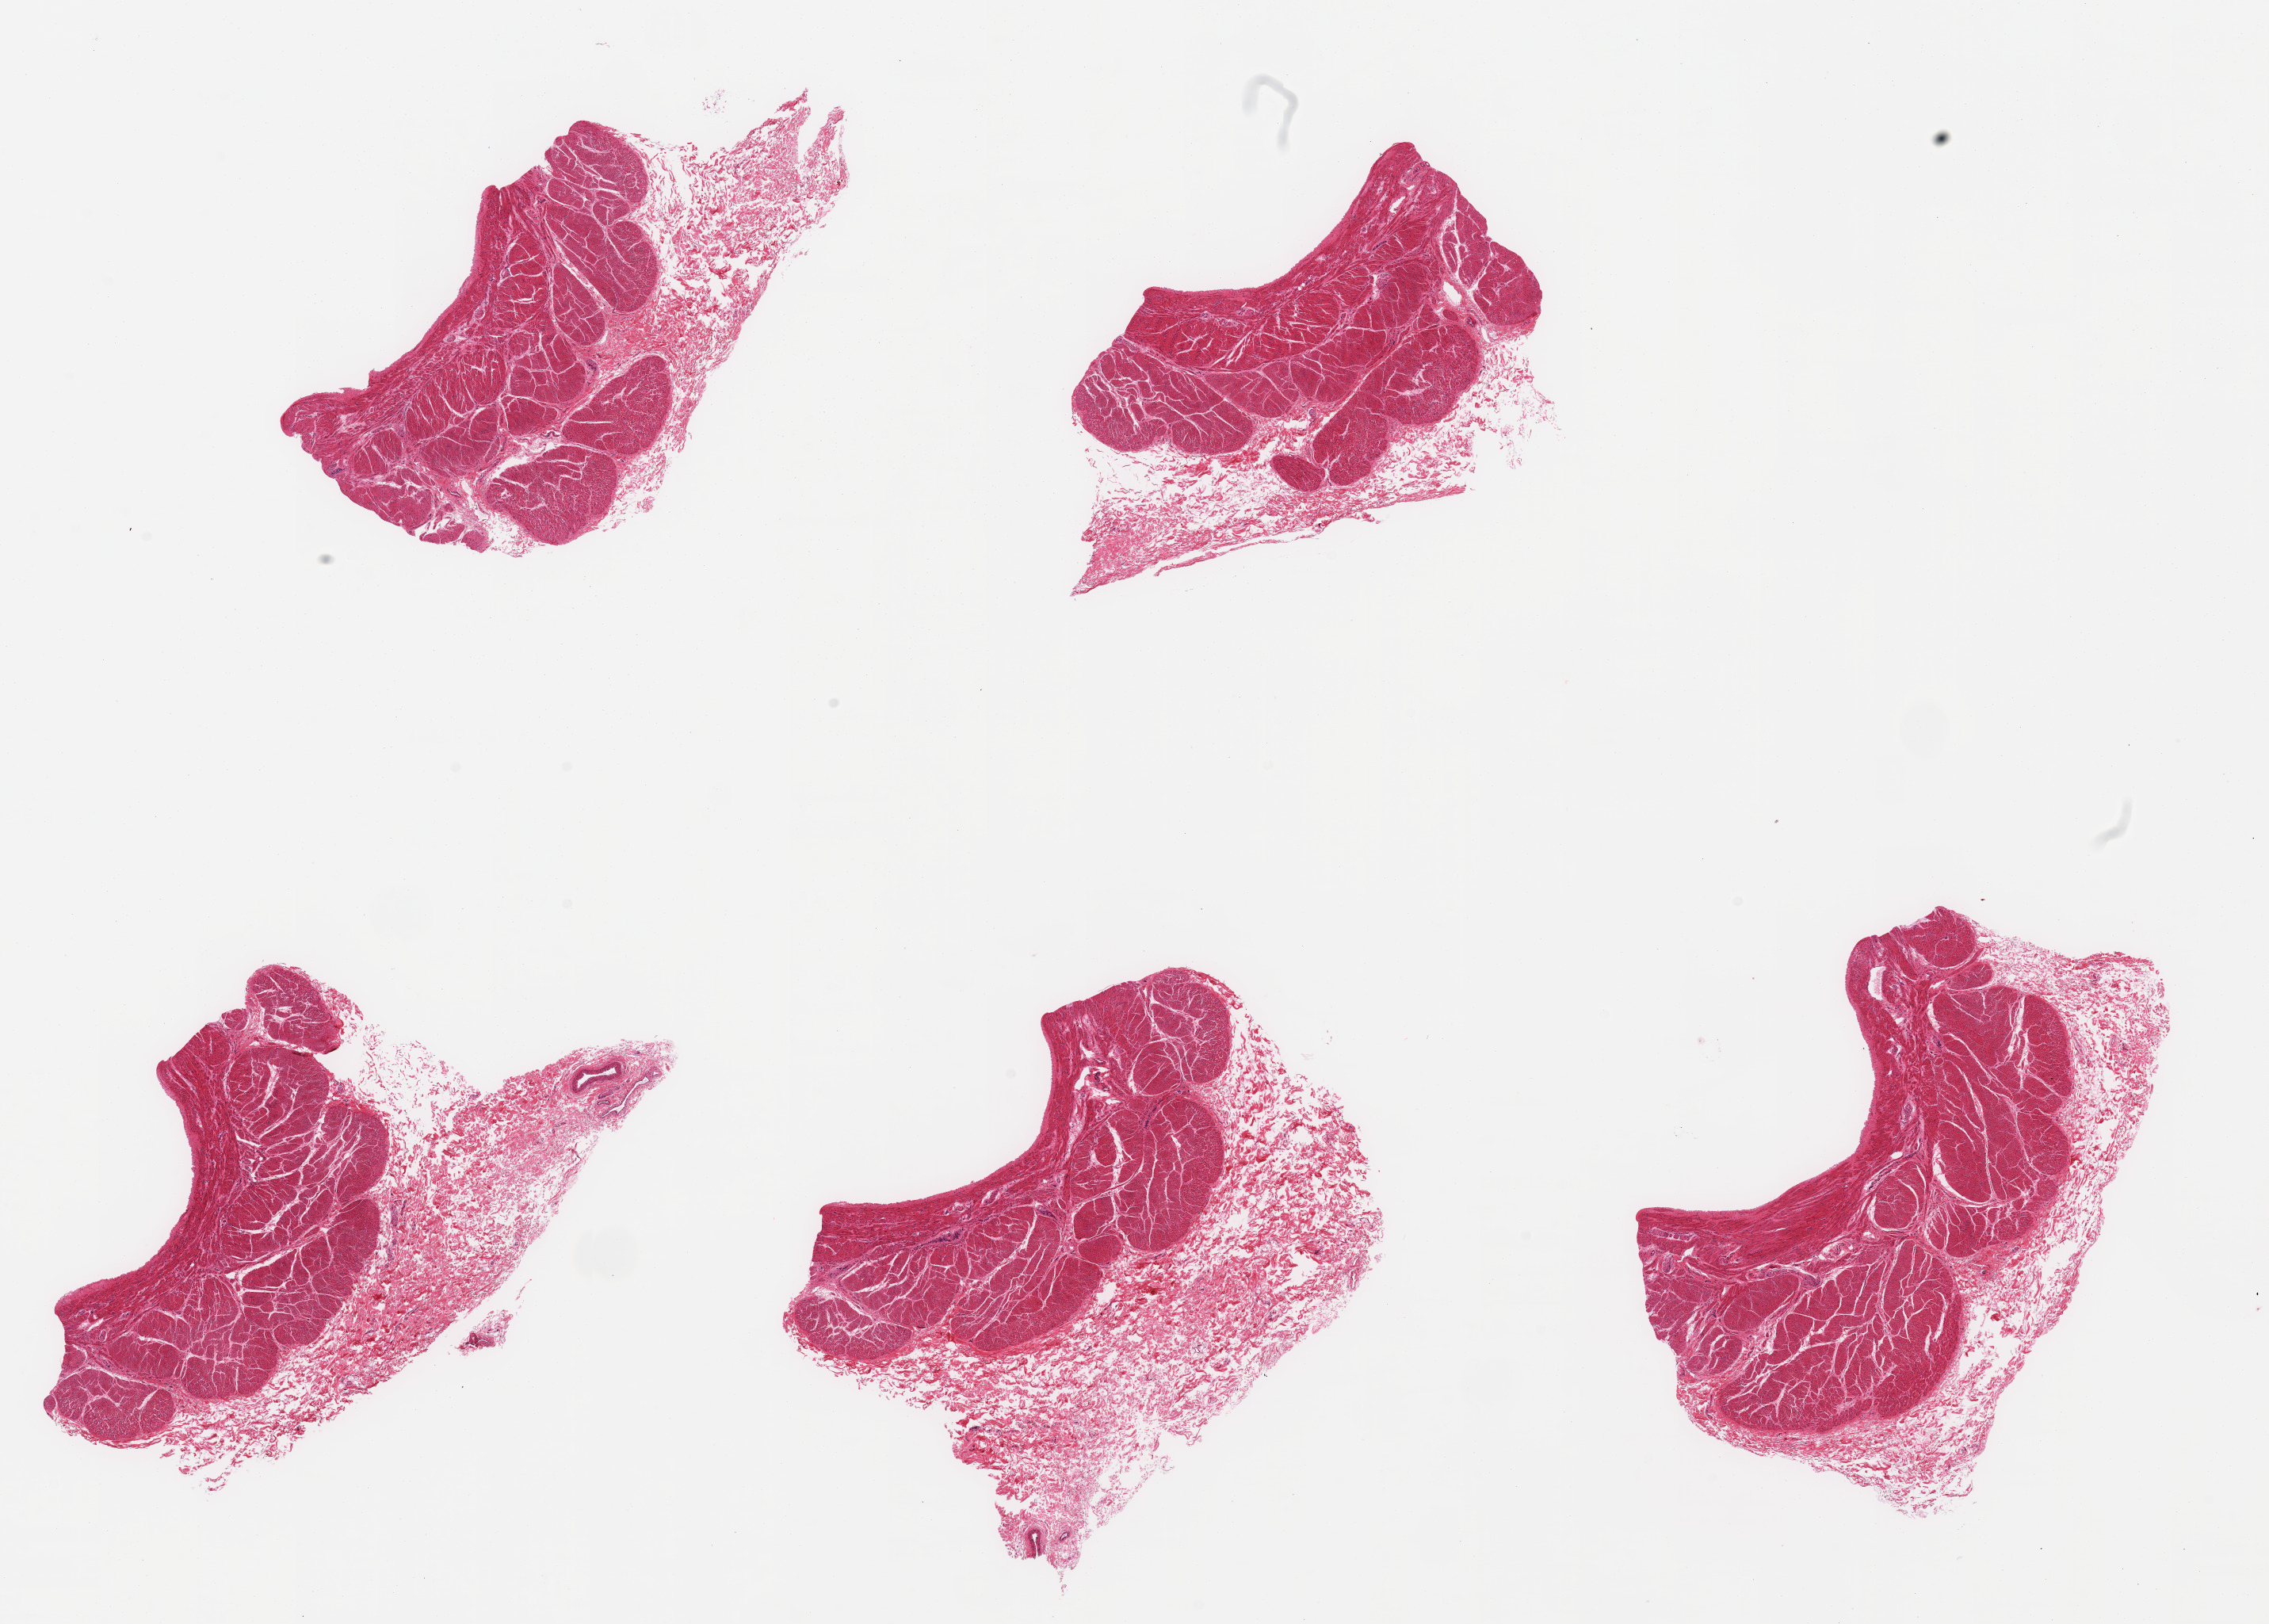
Whole-slide image, haematoxylin and eosin stain, brightfield, shown as a low-resolution overview of the whole scanned area (about 22.6 x 16.2 mm, acquisition: 20x scan); PAXgene-fixed, paraffin-embedded tissue; target tissue: stomach; donor tissue sample. Donor sex: female.
Reviewer comment on this tissue sample: 5 pieces, muscularis and serosa only, no target mucosa present.